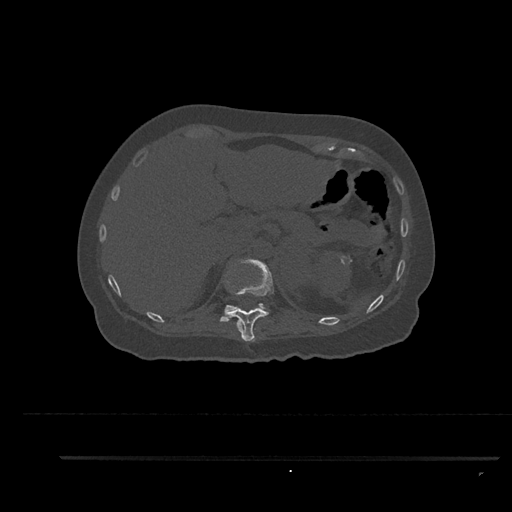
CT including the spine, one axial slice. Position 298 of 797 along the scan axis. Reconstruction kernel Br40s/3. 120 kVp. Bone window (W 1800 / L 400 HU). 0.5 mm slice thickness. 512 × 512 image matrix, field of view 408 × 408 mm. Female patient, age 44 years. Case-level facts recorded for this patient, not image findings: primary cancer: renal; vertebrae with lytic lesions (as recorded): L1.
Outlined on this slice (semi-automatic segmentation, software-assisted and operator-edited):
- T11 vertebra: bounding box [x1, y1, x2, y2] px = [228, 259, 274, 342]
- T12 vertebra: [220, 303, 268, 322]